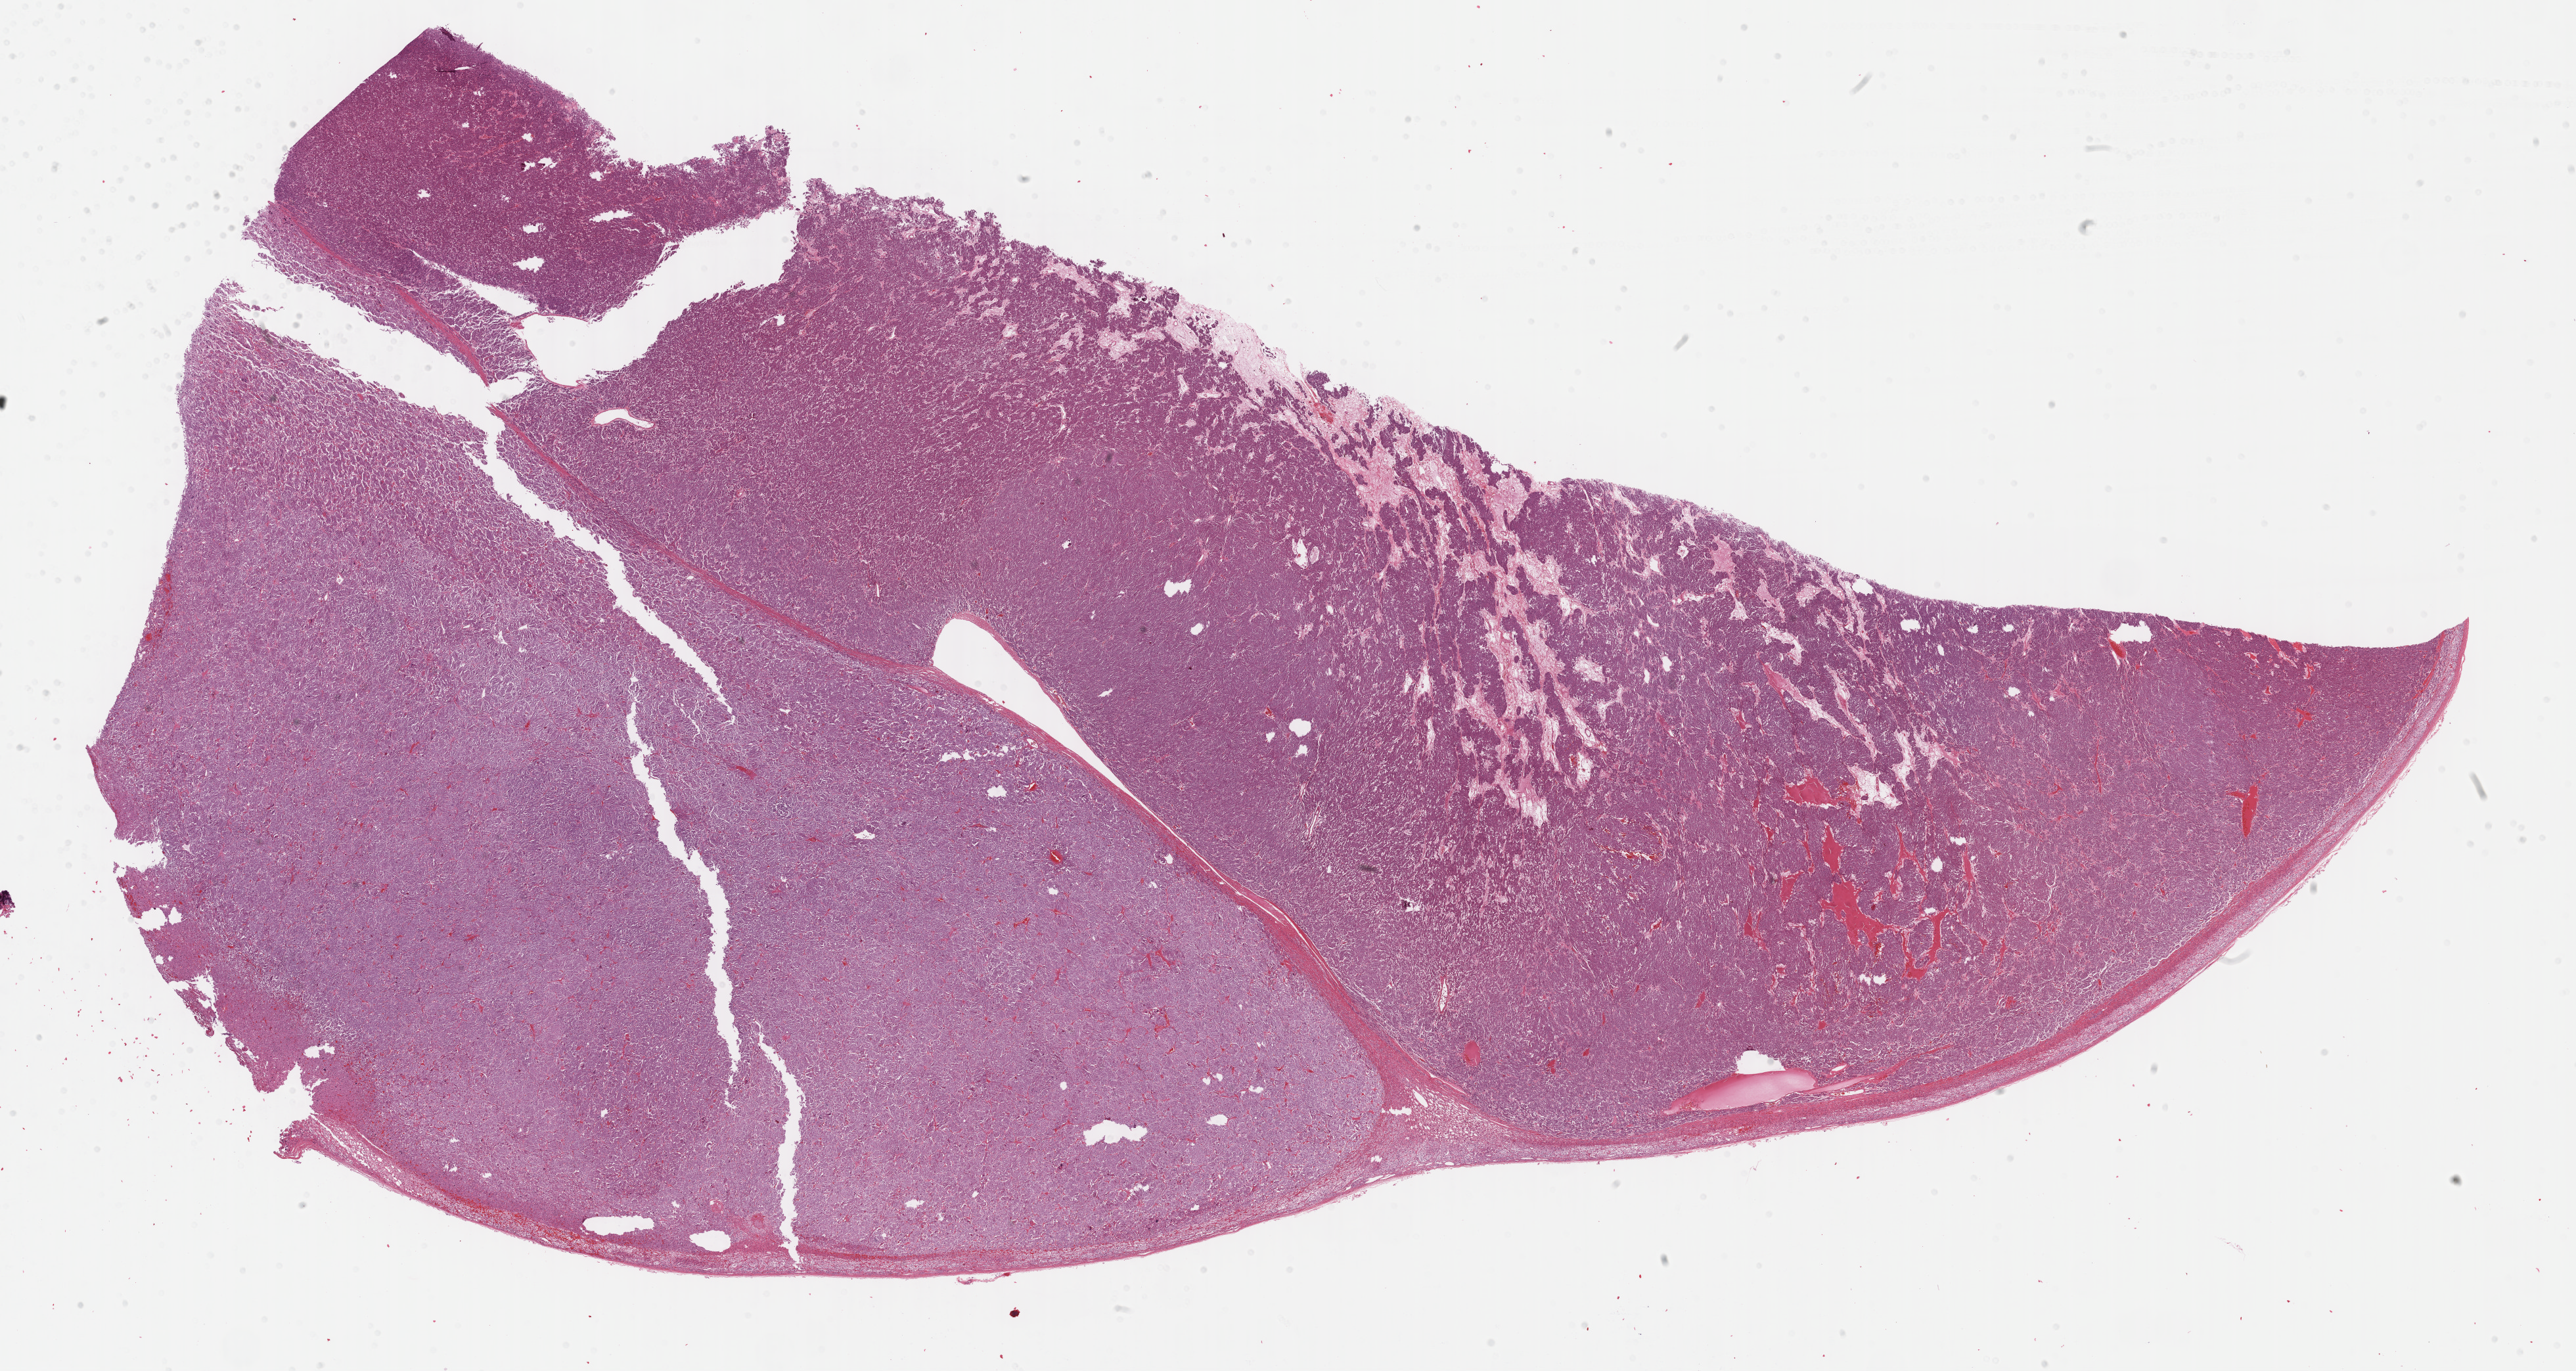
H&E-stained whole-slide image, whole scanned area (about 31.7 x 16.9 mm, acquisition: 40x scan) shown as a low-resolution overview. Formalin-fixed paraffin-embedded (FFPE) diagnostic section. Adrenal gland, primary tumour sample. Female, age 28 years at initial diagnosis.
Pathologic diagnosis: Medullary carcinoma, NOS (thyroid gland). AJCC pathologic stage: IVA (7th edition). Laterality: bilateral. TNM: T2 N1b MX.